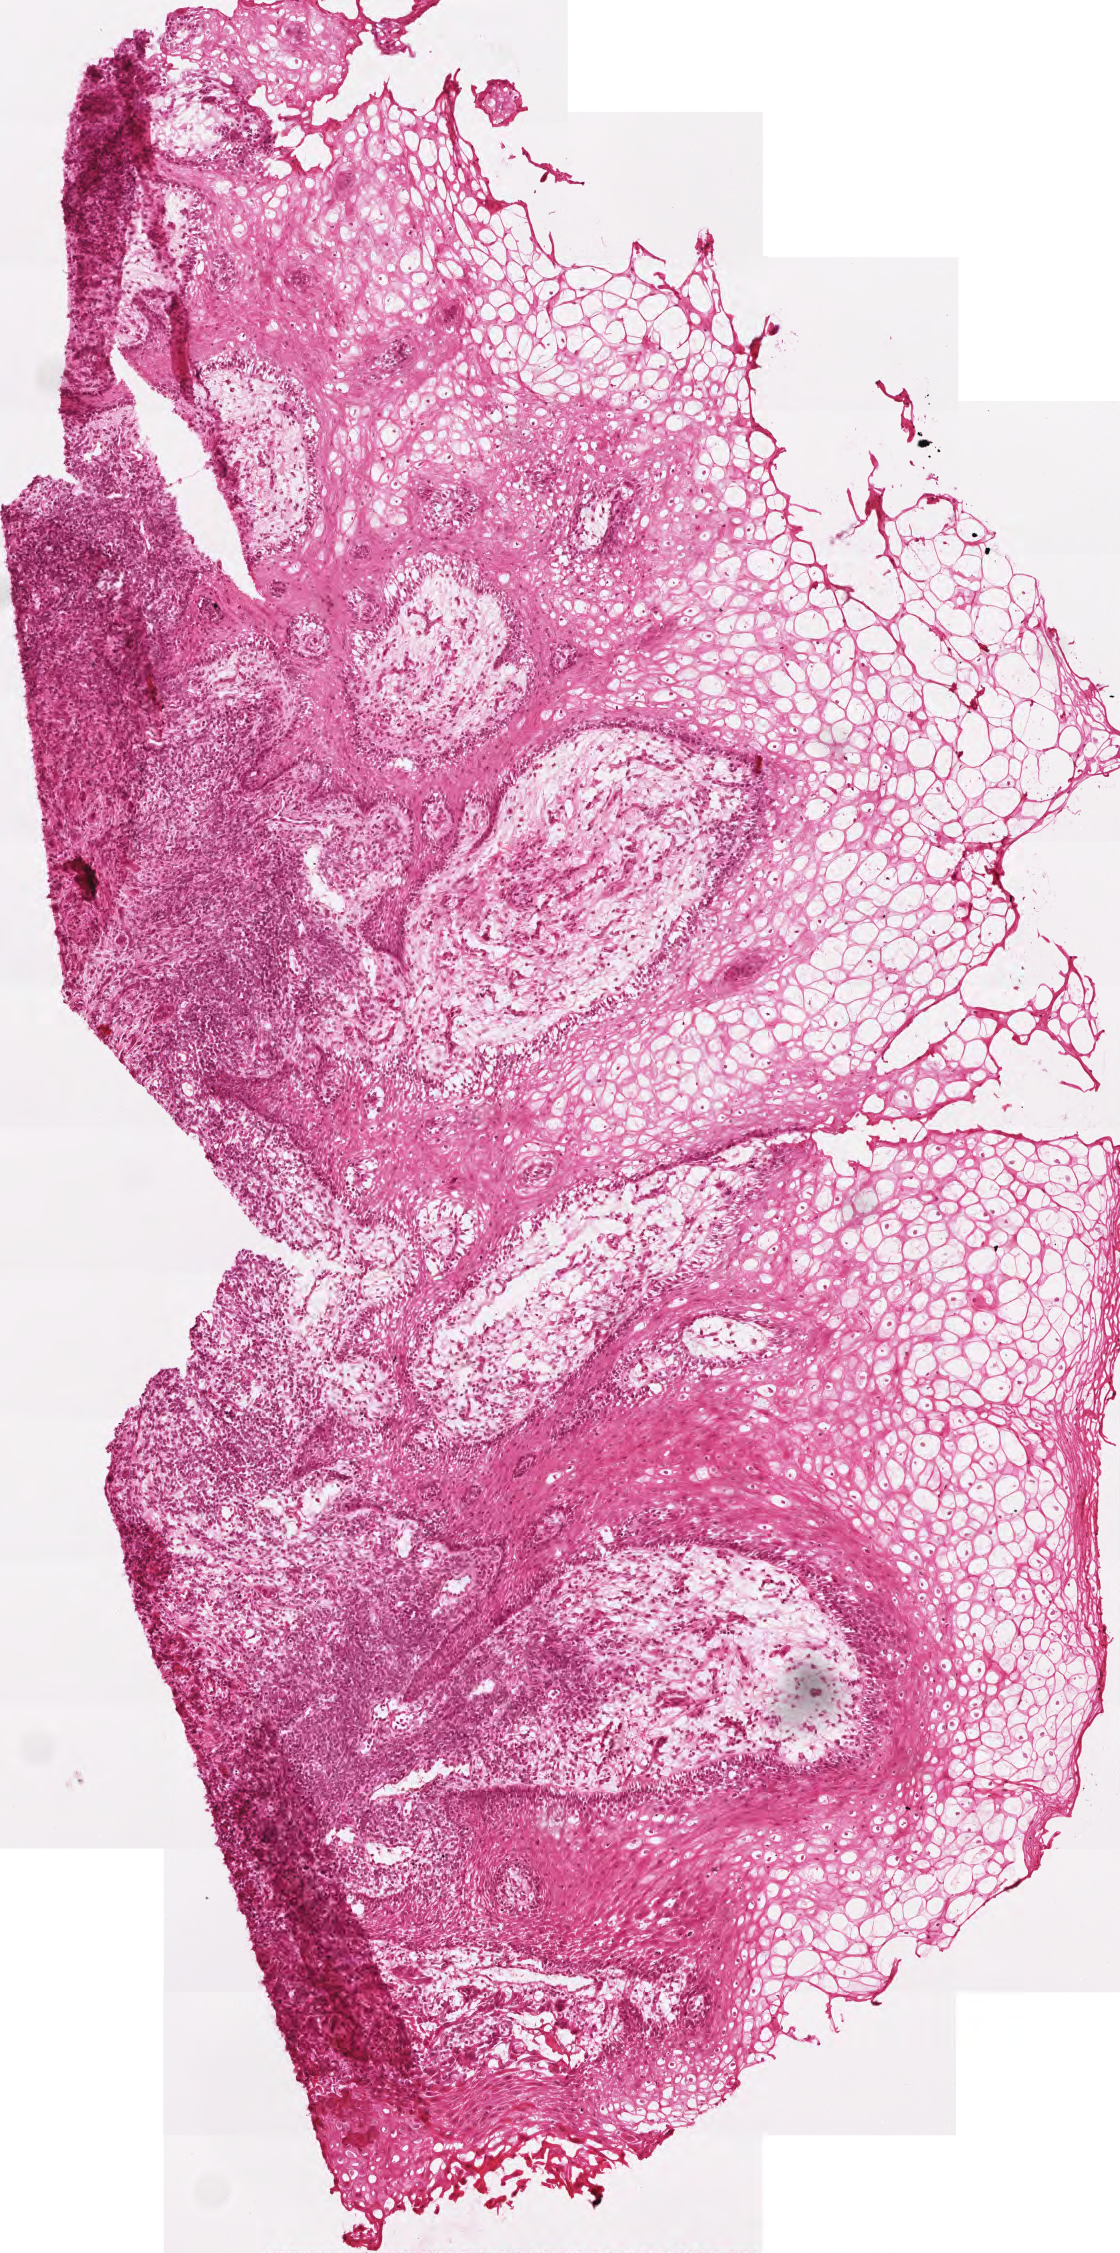
Digitized H&E-stained tissue section (whole slide) — low-resolution overview of the scanned area, about 2.2 x 4.5 mm, frozen section from the top of the tissue portion, head and neck, primary tumour sample. Male, age 26 years at initial diagnosis. Histologic grade: G2 (moderately differentiated). Slide review estimates, as recorded: tumour cells 75%, tumour nuclei 60%, normal cells 0%, stromal cells 25%, necrosis 0%. Inflammatory infiltration, as recorded: lymphocyte infiltration 35%, monocyte infiltration 0%, neutrophil infiltration 0%.
AJCC pathologic stage: III. Lymph nodes positive (case pathology): 1 of 44 examined. Histologic diagnosis: Squamous cell carcinoma, NOS (tongue, NOS). Laterality: right.